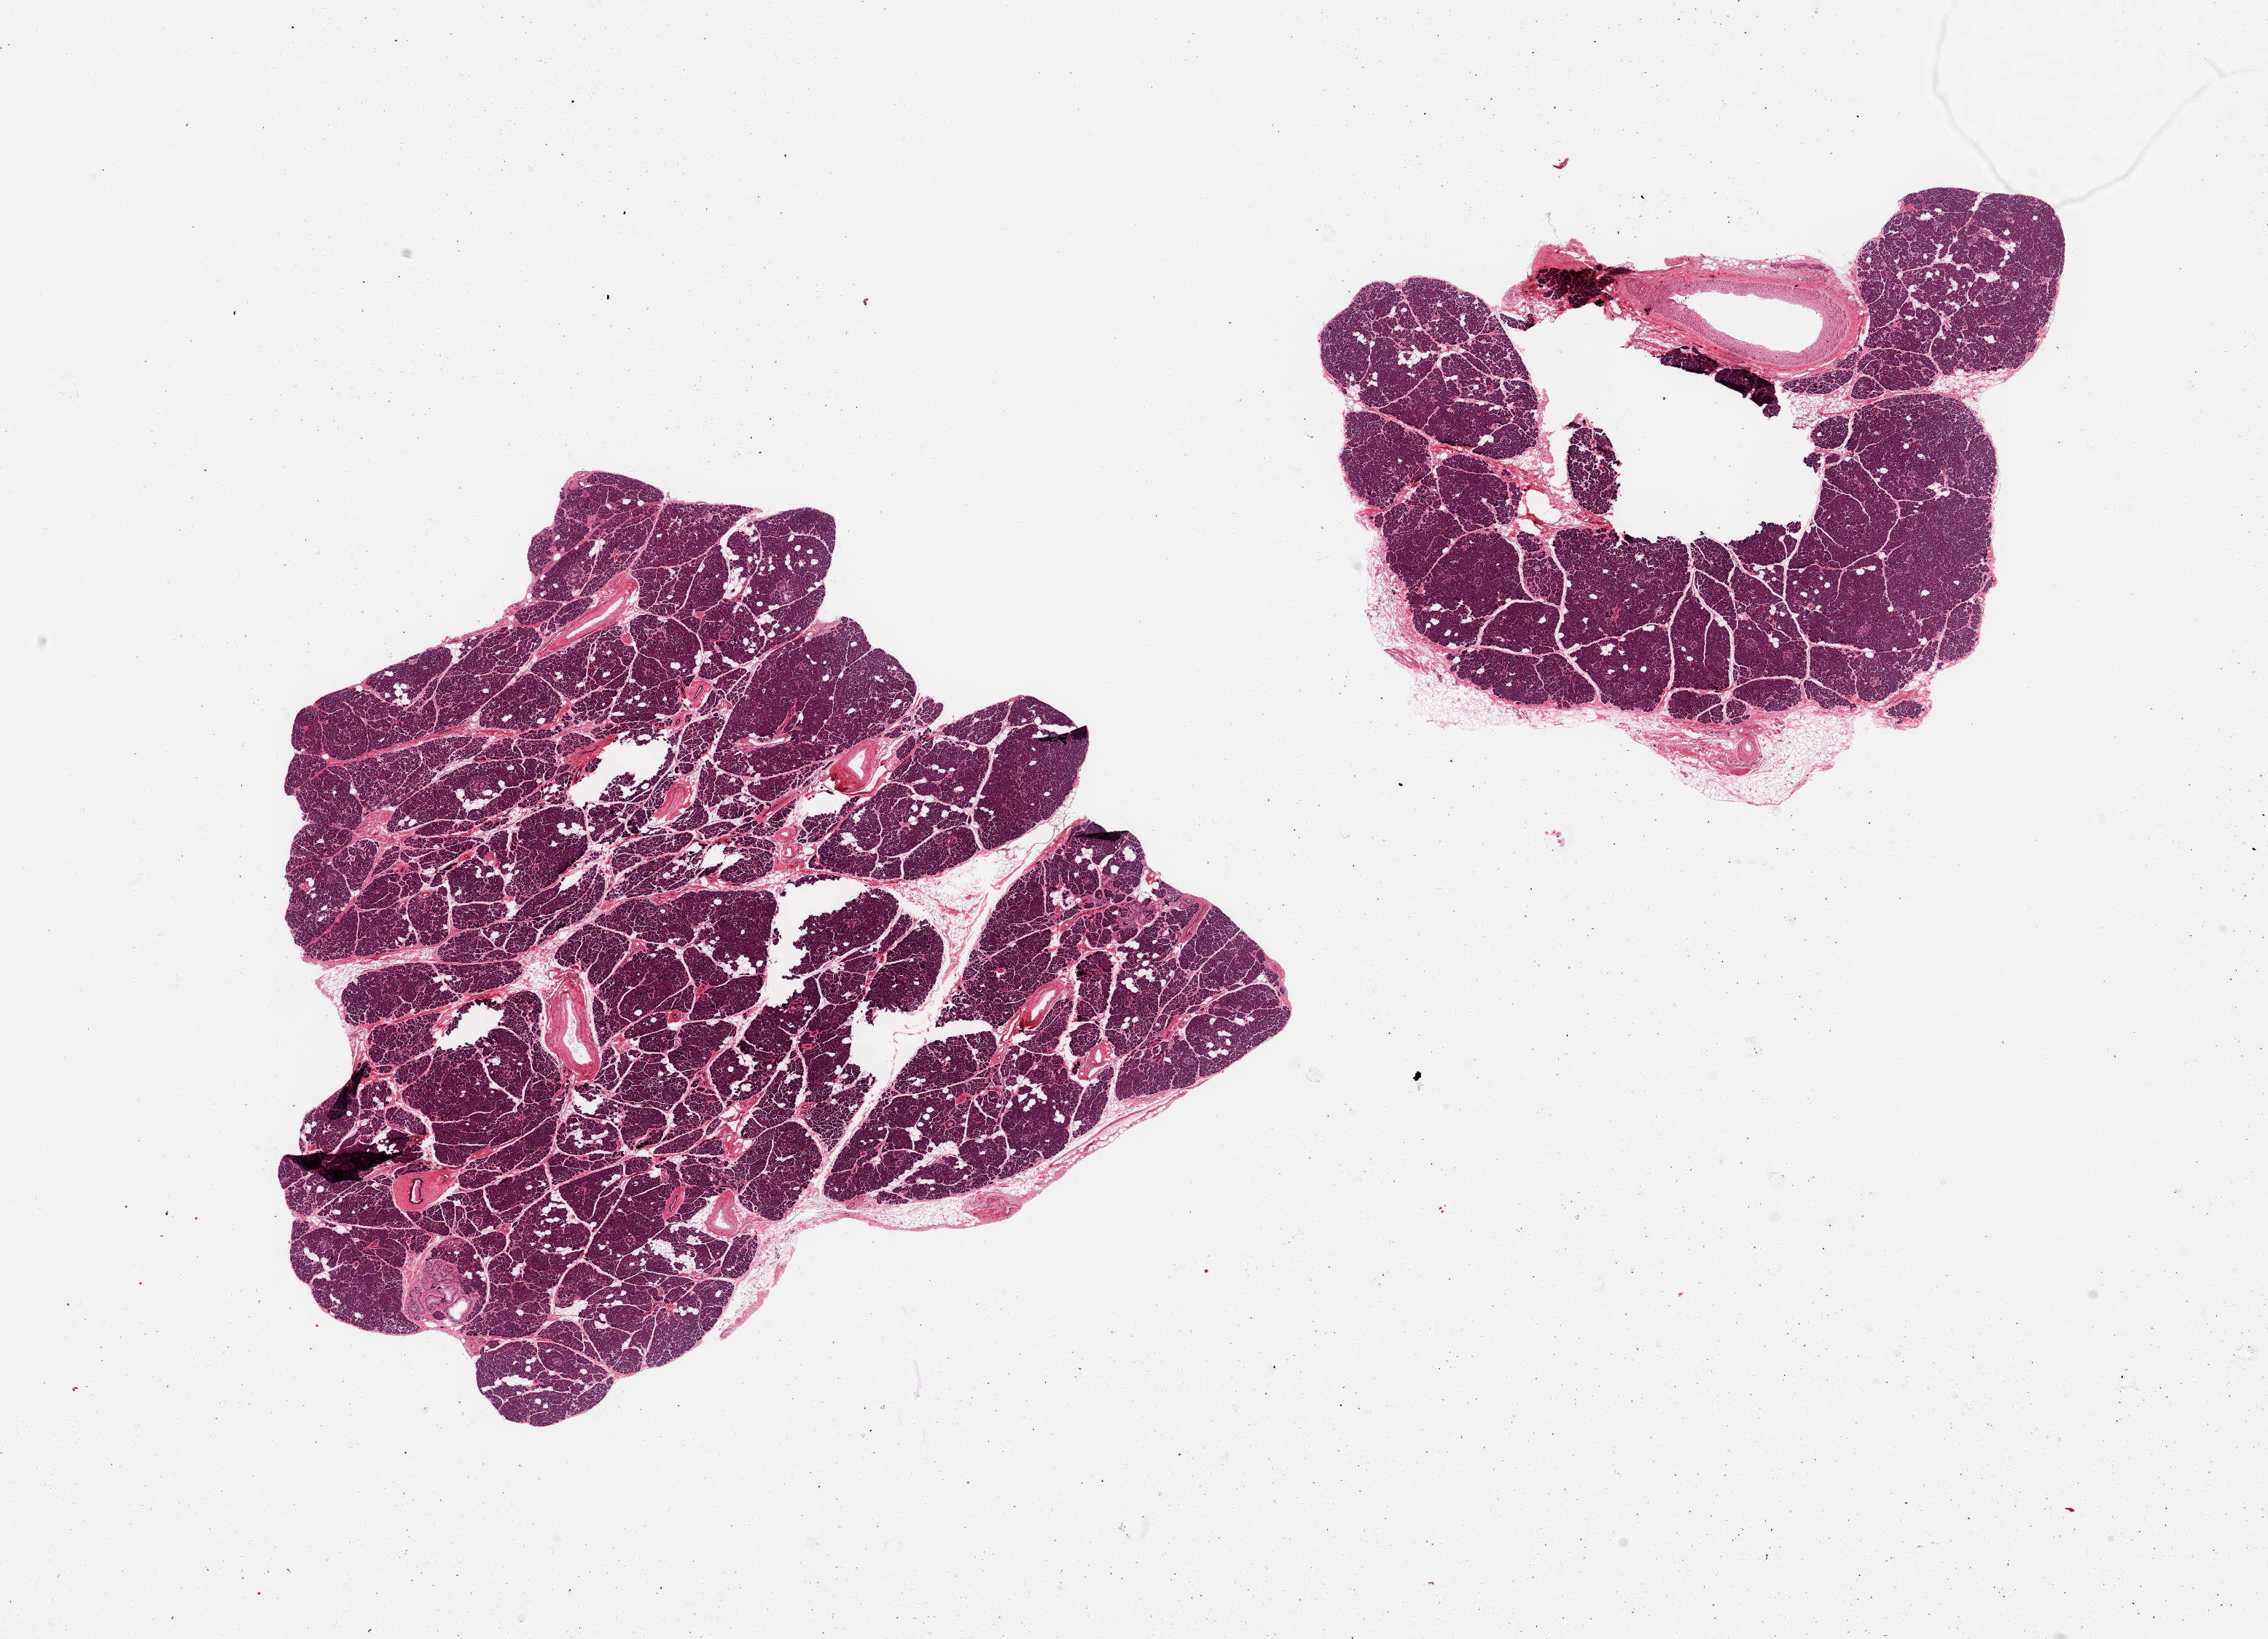
H&E whole-slide image — whole scanned area (about 24.6 x 17.8 mm) shown as a low-resolution overview. PAXgene-fixed paraffin-embedded (PFPE) section. Target tissue: pancreas. Donor tissue sample. Donor: female.
- review note (as recorded): 2 pieces, well-preserved, Islets well visualized